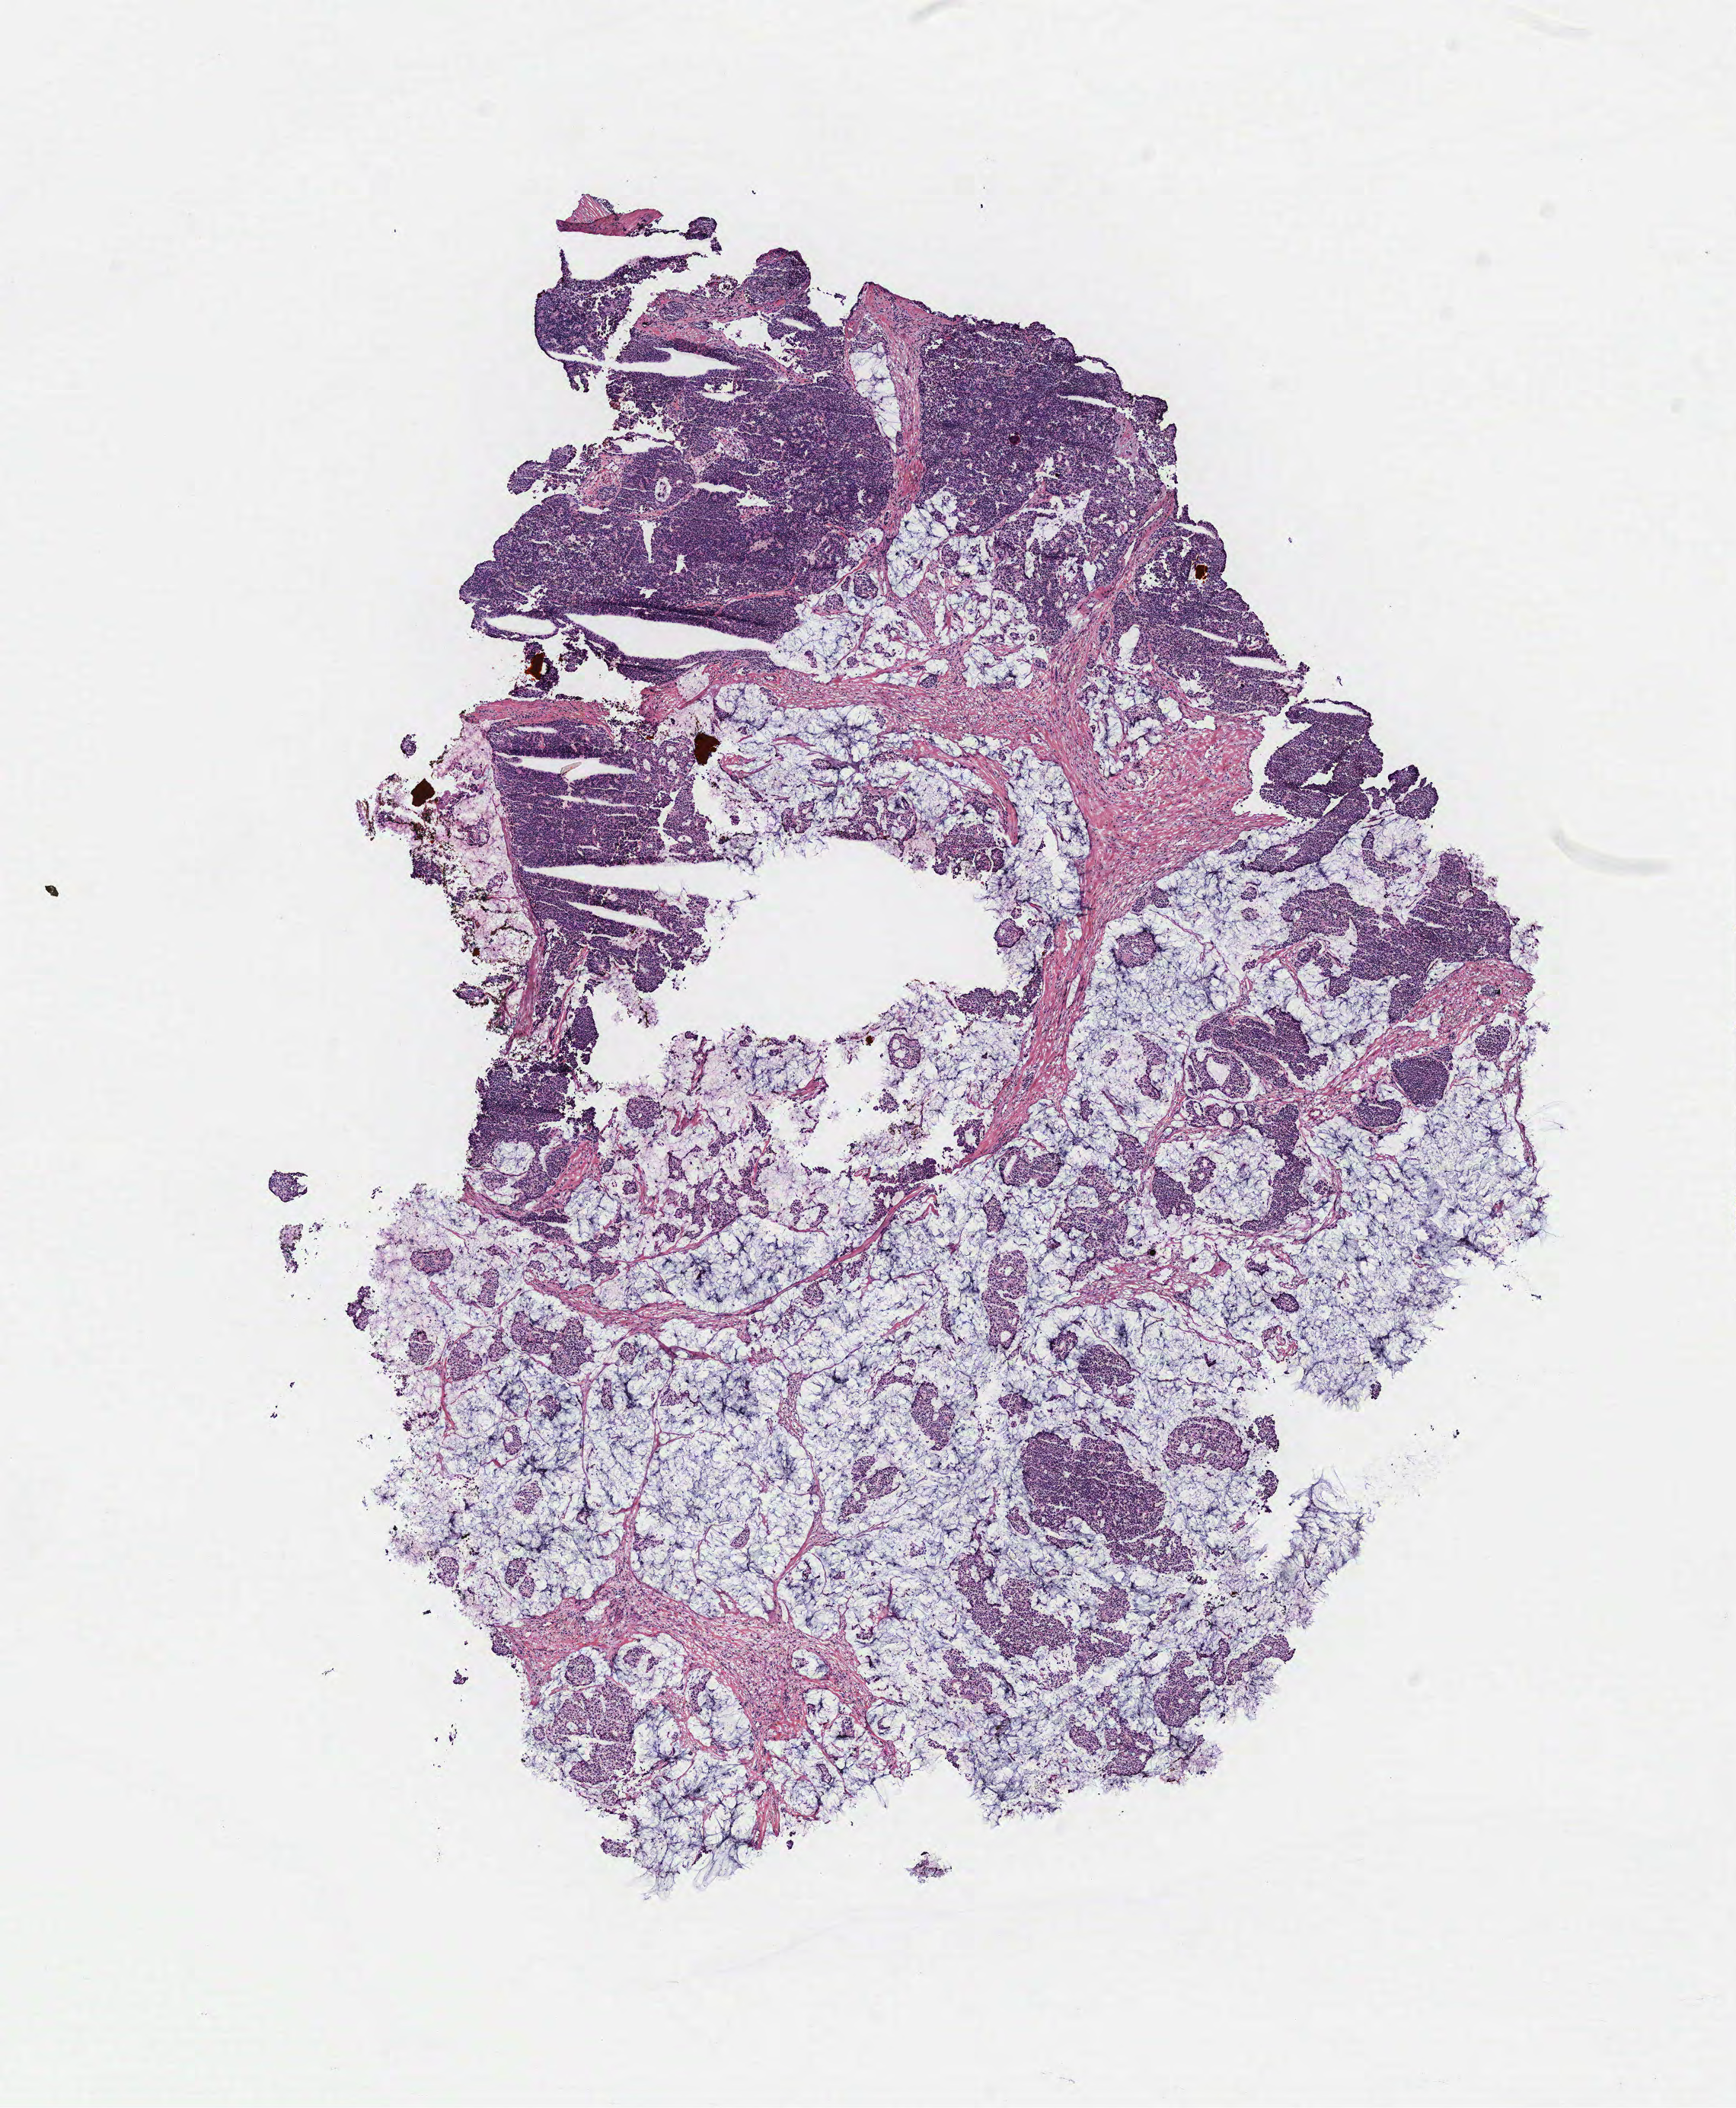
H&E whole-slide image — shown as a low-resolution overview of the whole scanned area (about 9.1 x 11.1 mm, acquisition: 40x scan), breast, tumour tissue. Patient: female, age 82 years.
AJCC pathologic stage: IIA. Histologic diagnosis: Infiltrating duct carcinoma, NOS.